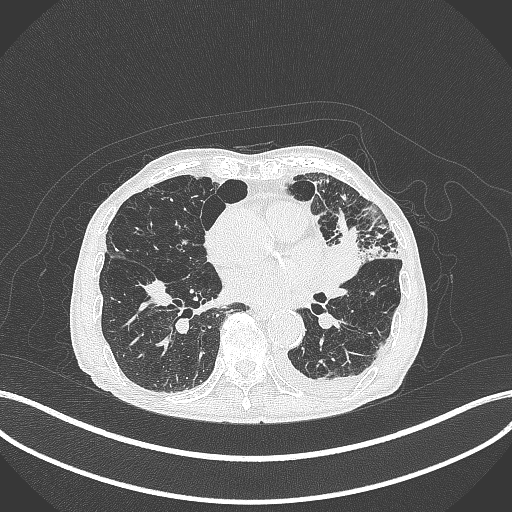
Chest CT, one axial slice; slice 167 of 385 in the series (ordered by position); lung window (W 1500 / L -600 HU); 1 mm slice thickness; 512 × 512 image matrix. Male patient, age 90 years or older. Case-level facts recorded for this patient, not image findings: clinical TNM (as recorded): T2b N1 M0.
Structures marked on this image (bounding box drawn by a radiologist):
- lung tumour (recorded histology: squamous cell carcinoma): box from (x=332, y=230) to (x=367, y=278) px